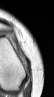
MRI of an extremity soft-tissue mass, one axial slice; position 12 of 42 along the scan axis; MR volume resampled by the dataset authors to the PET/CT grid (not the native acquisition matrix); 3.27 mm slice thickness; 54 × 97 image matrix. Female patient. Case-level facts recorded for this patient, not image findings: histological type: spindle cell suggestive of biphasic synovial sarcoma; grade: intermediate; site of the primary tumour: left knee.
Structures marked on this image (expert contour drawn on MRI and transferred to this co-registered scan by the dataset authors):
- gross tumour volume including surrounding oedema: bounding box <21,57,27,65> (left, top, right, bottom; pixels)